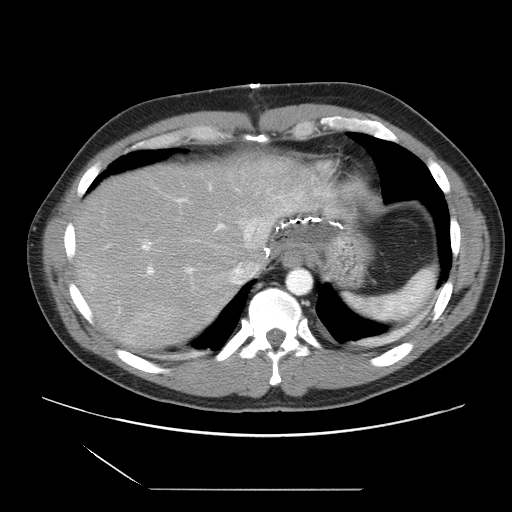
Contrast-enhanced abdominal CT, one axial slice. Slice 26 of 39 in the series (ordered by position). 120 kVp. Intravenous contrast given. Soft-tissue window (W 400 / L 40 HU). 5 mm slice thickness. 512 × 512 image matrix, field of view 395 × 395 mm. Male patient, age 39 years. Case-level facts recorded for this patient, not image findings: diagnosis: colorectal cancer liver metastases, imaged before liver resection; multiple liver metastases: yes; largest metastasis: 1.3 cm; disease in both lobes: no.
Annotated regions visible in this slice (manually delineated by an expert):
- hepatic veins: bounding box <189,243,258,290> (left, top, right, bottom; pixels)
- liver: <73,154,339,349>
- planned liver remnant (the part of the liver to remain after resection): <119,155,338,263>
- portal vein (with intrahepatic branches): <107,198,257,314>